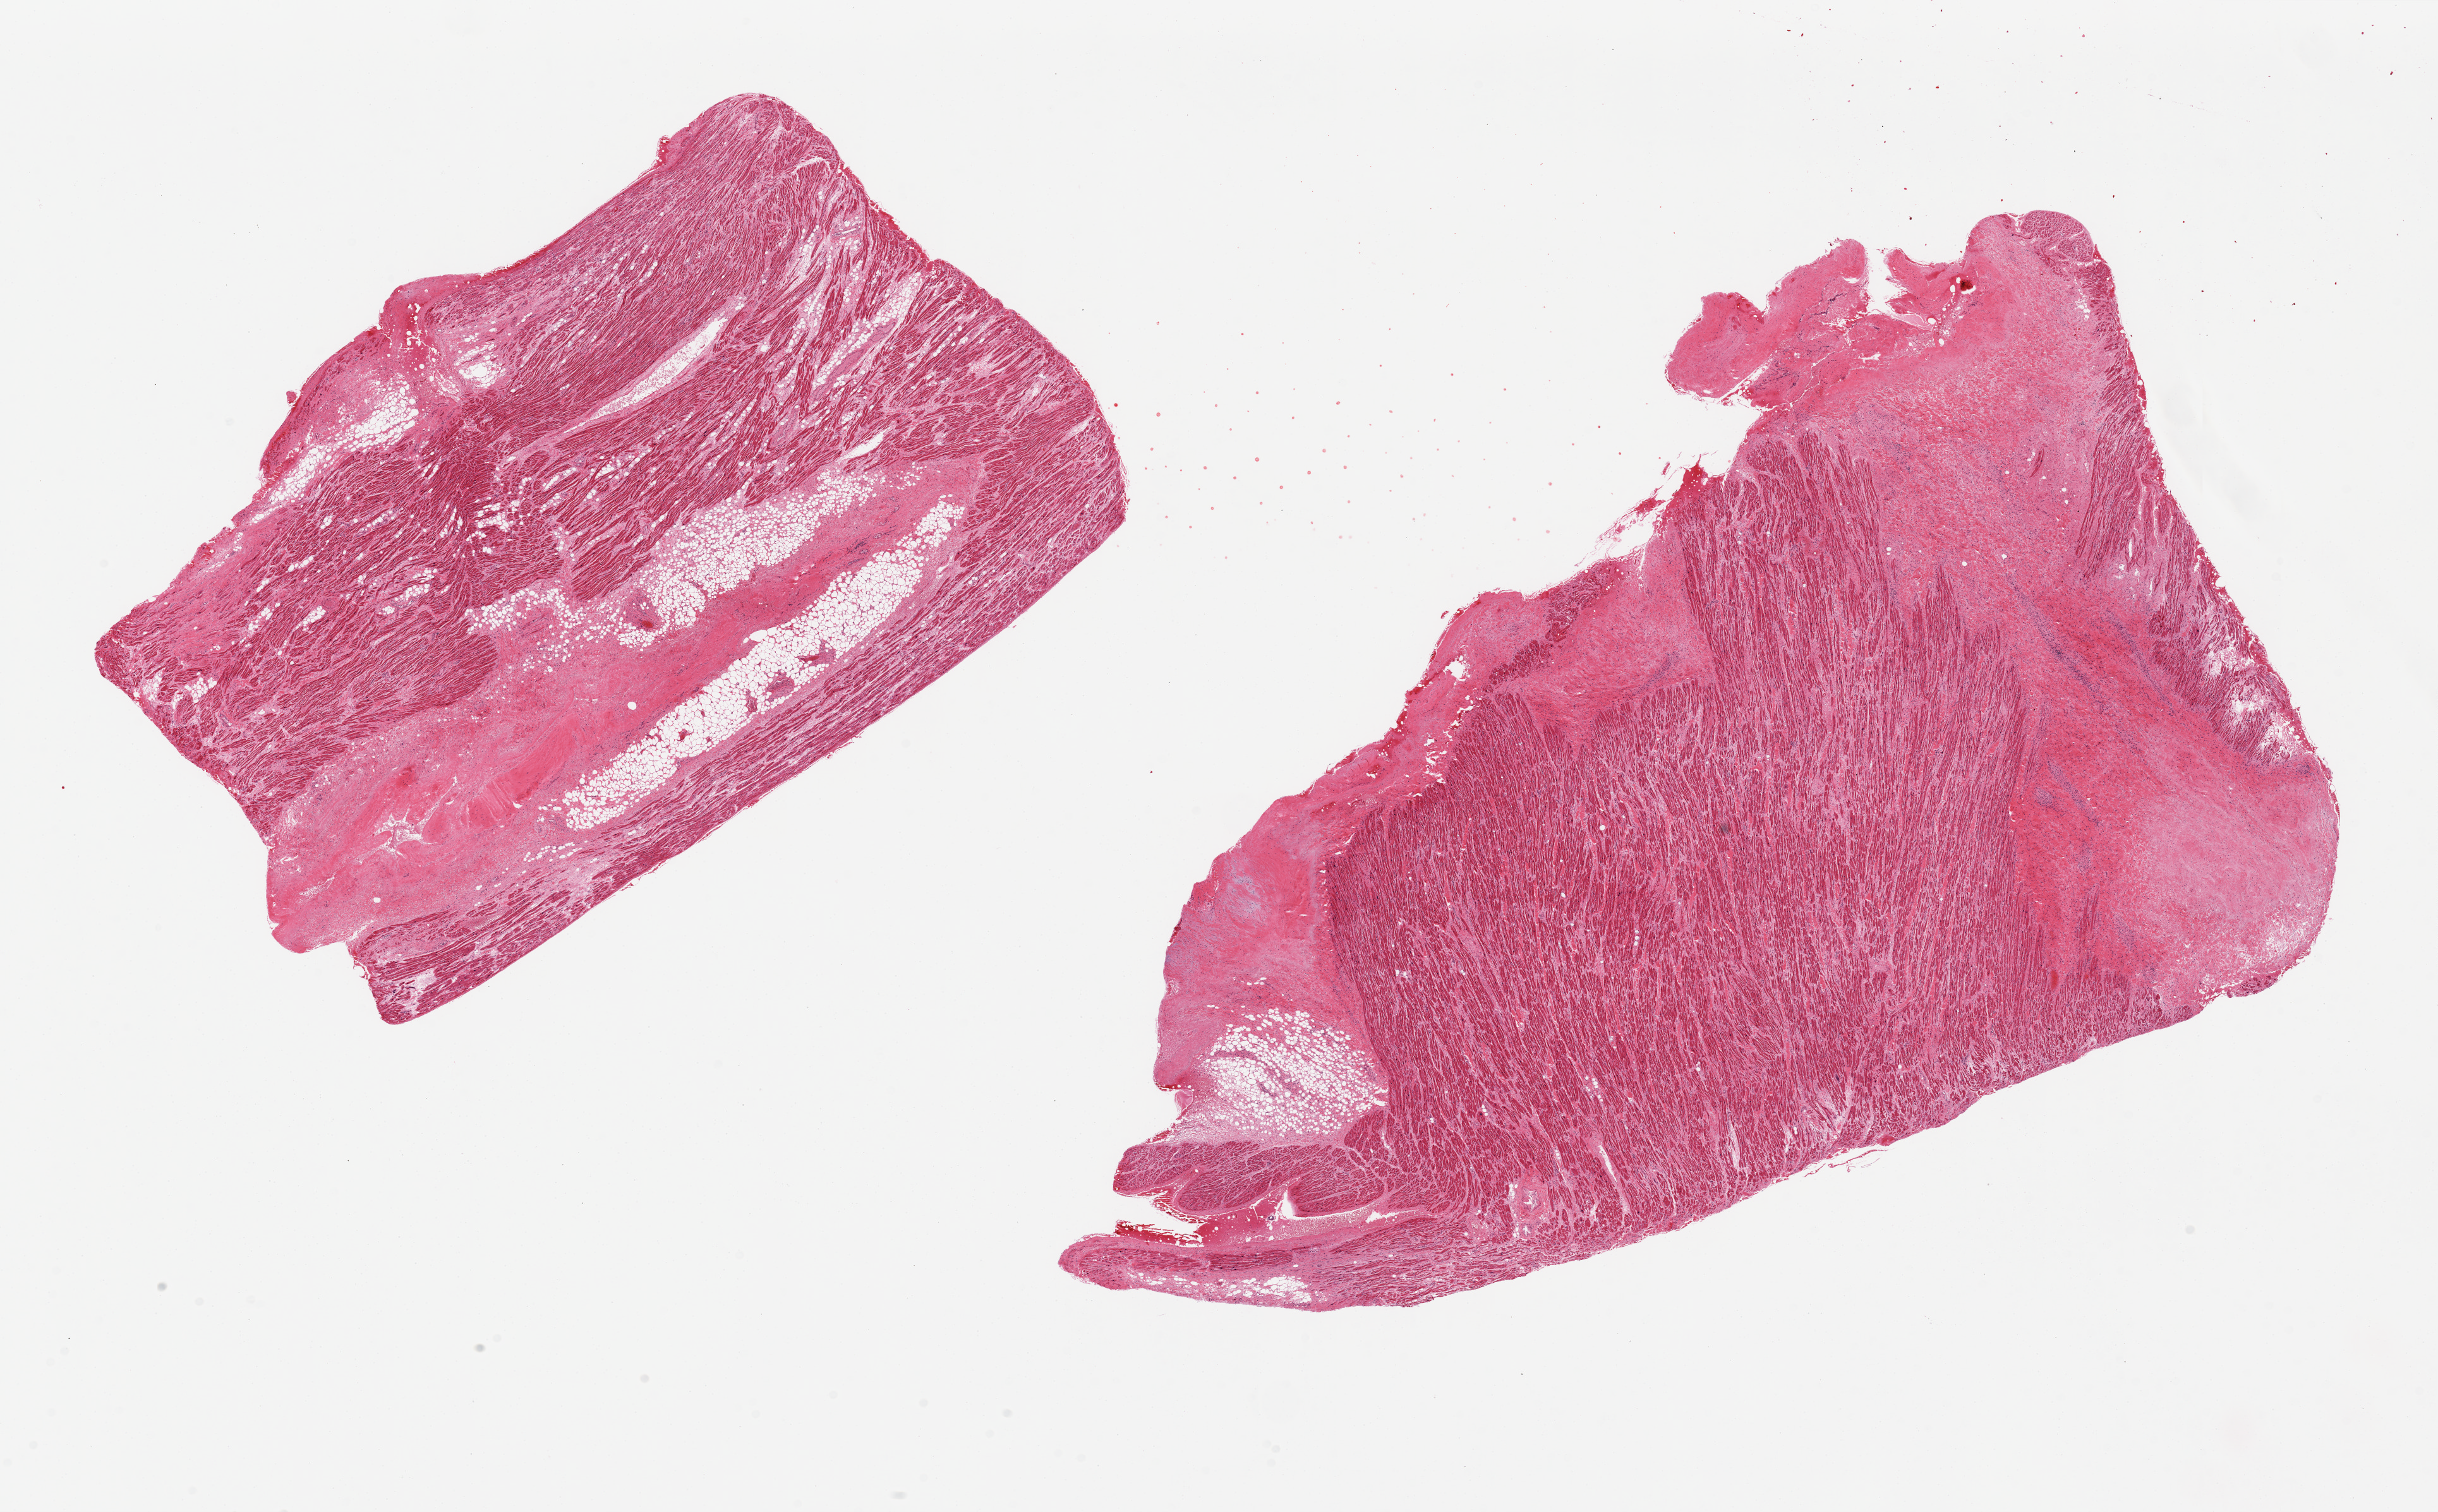
Whole-slide image, haematoxylin and eosin stain — a low-resolution overview of the entire scanned area, about 30.5 x 18.9 mm. PAXgene-fixed paraffin-embedded (PFPE) section. Sampled site (target tissue): auricular appendage. Donor tissue sample.
Pathologist's review note for this sample: 2 pieces, 20-30% fibrosis, fatty infiltration.